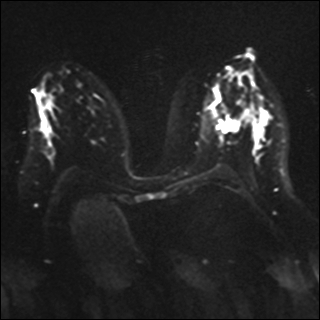
Breast MRI, one axial slice; position 19 of 41 along the scan axis; diffusion-weighted series; image 2 of 4 stored at this slice position (different b-values; order by instance number); 1.5 T; 320 × 320 image matrix, field of view 340 × 340 mm. Female patient.
Annotated regions visible in this slice (outlined manually by an expert reader):
- tumour on diffusion-weighted imaging: bounding box <216,118,237,133> (left, top, right, bottom; pixels)